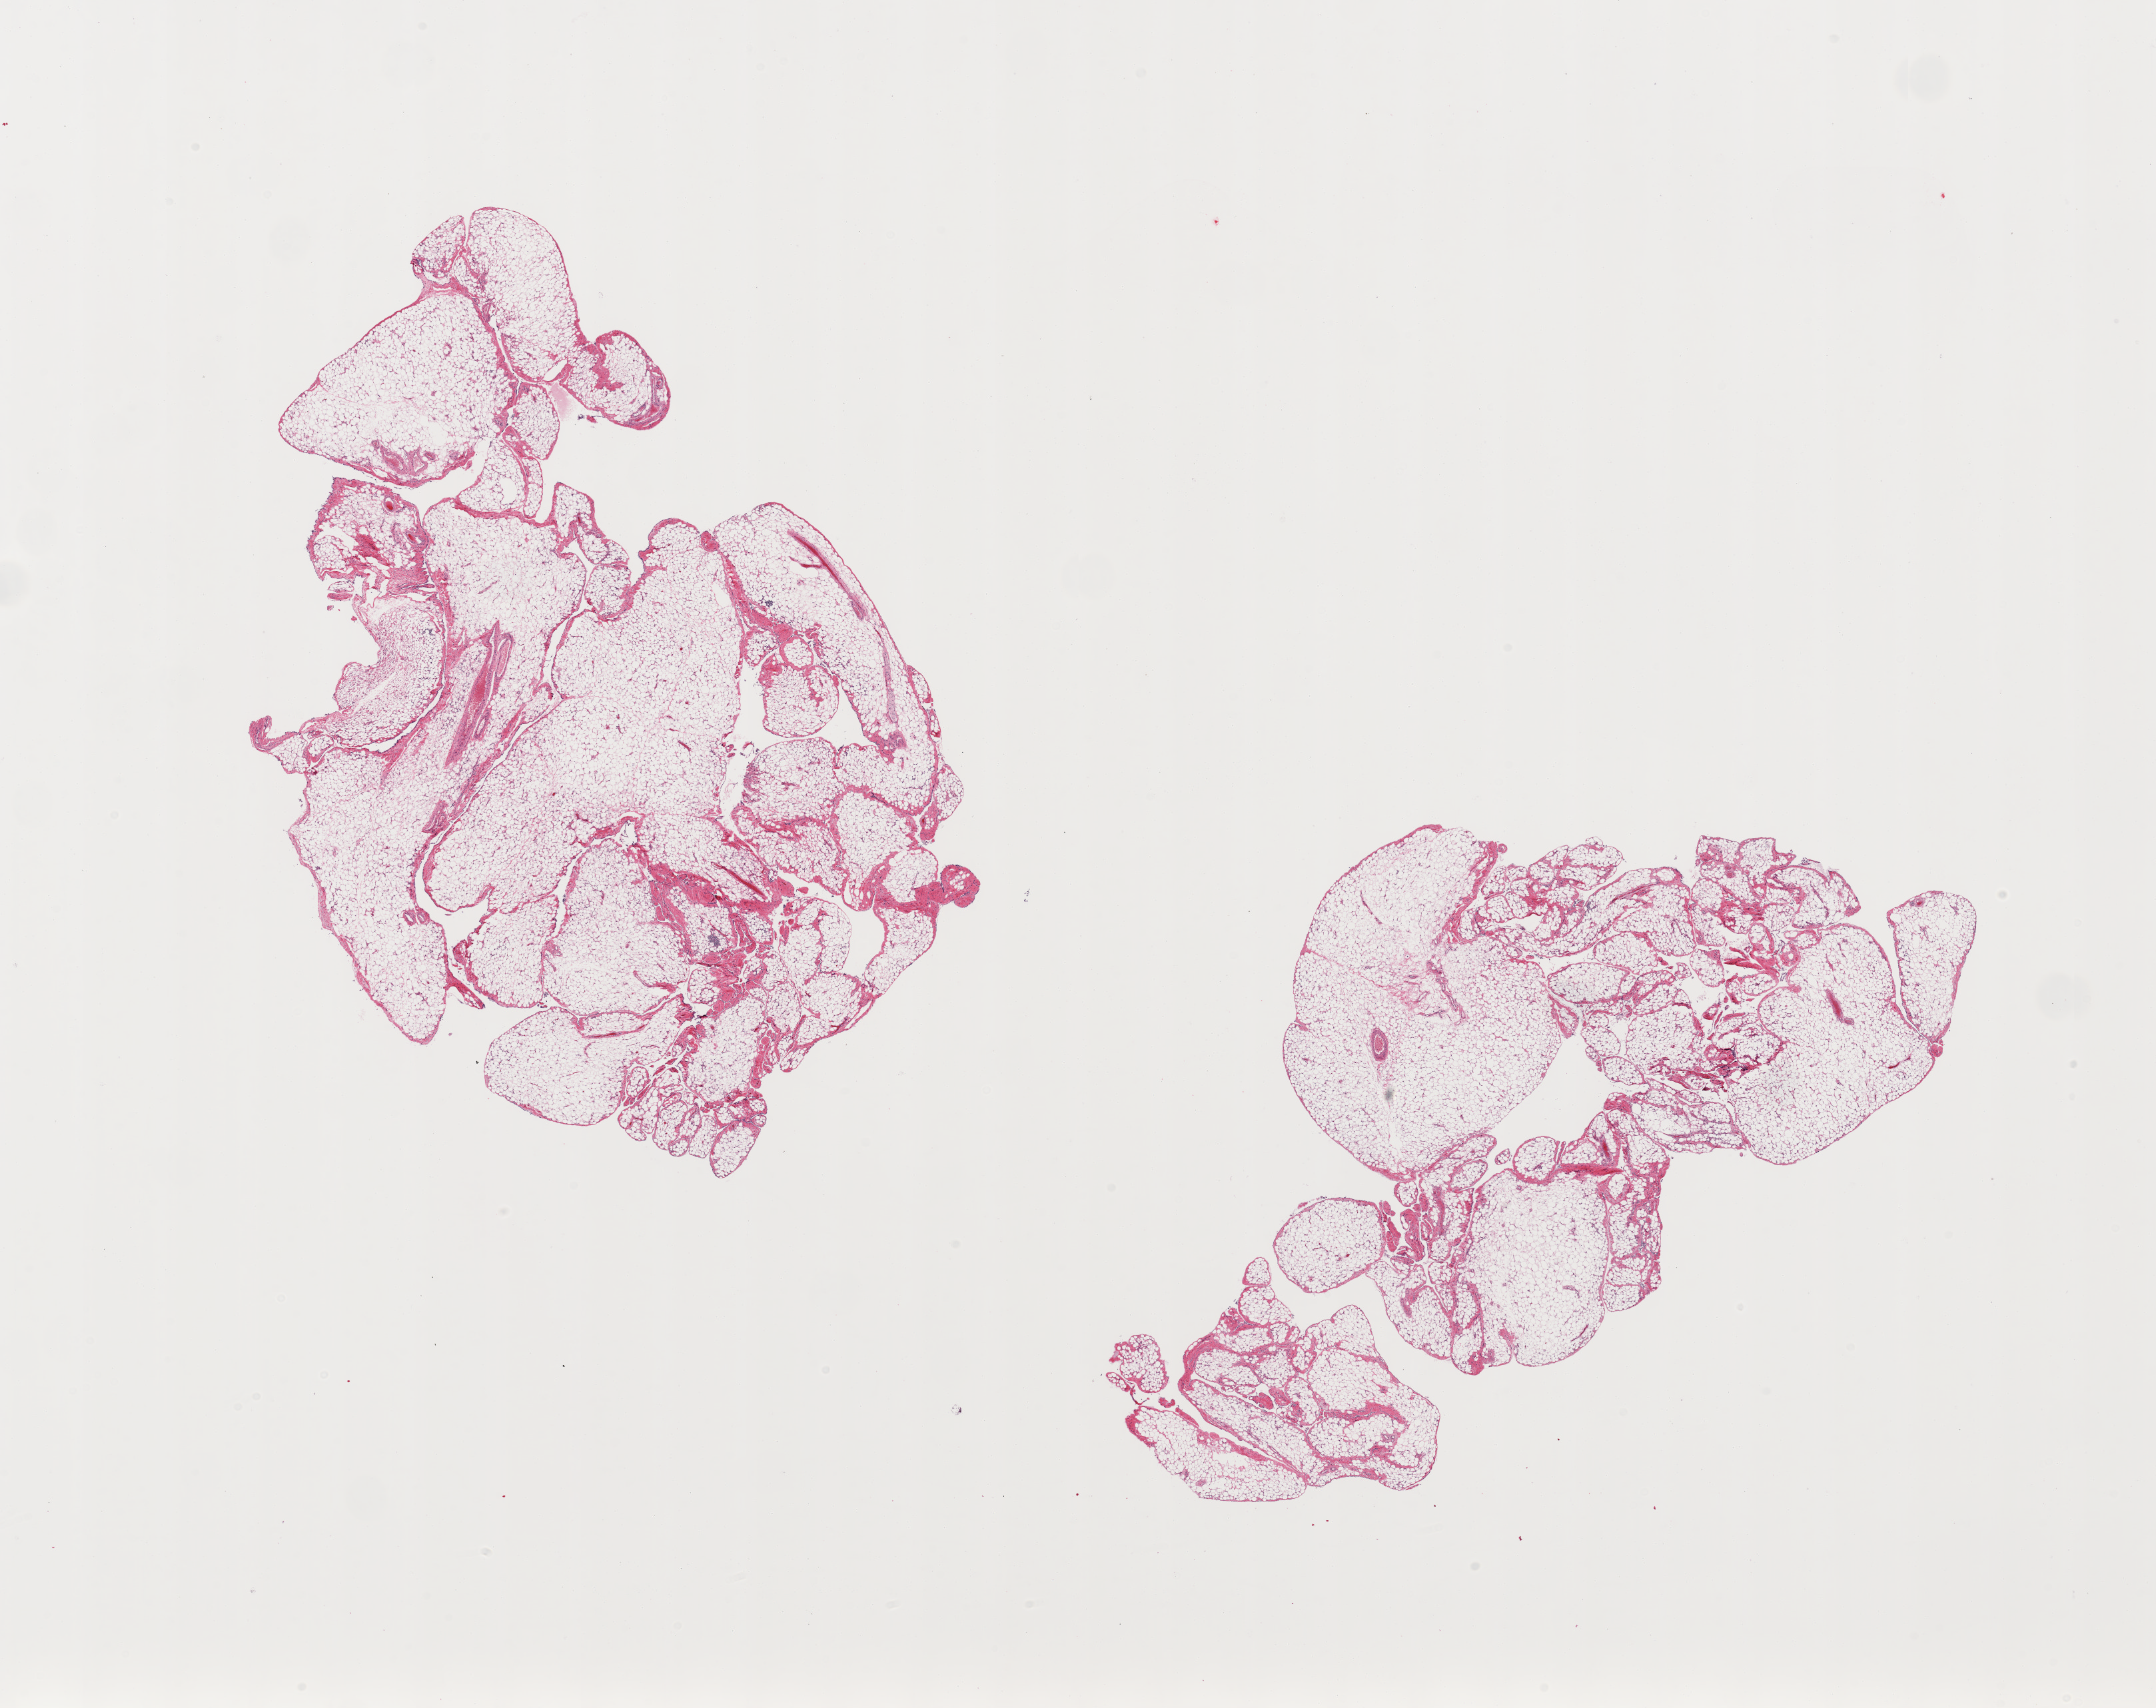
Whole-slide image, hematoxylin and eosin (H&E) stain, brightfield, a low-resolution overview of the entire scanned area, about 25.6 x 20.3 mm; PAXgene-fixed, paraffin-embedded tissue; sampled site (target tissue): omentum; donor tissue sample. Donor: male.
Review note (as recorded): 2 pieces; lobulated mature adipose tissue with fibrovascular component.